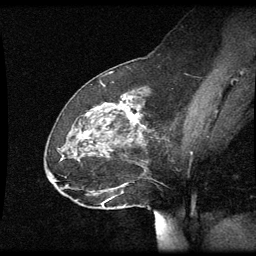
Breast MRI (dynamic contrast-enhanced), one sagittal slice; position 25 of 60 along the scan axis; dynamic contrast-enhanced series, image 2 of 3 at this slice position (ordered by acquisition); 1.5 T; TE 4.2 ms, TR 8.9 ms; 2 mm slice thickness; 256 × 256 image matrix, field of view 200 × 200 mm. Female patient, age 49 years. Case-level facts recorded for this patient, not image findings: setting: breast cancer imaged before/during neoadjuvant chemotherapy; receptor status: HR-positive, HER2-negative.
Structures marked on this image (semi-automatic segmentation, software-assisted and operator-edited):
- analysis volume of interest (the breast-tissue region the enhancement analysis was run in; not a lesion): box from (x=46, y=92) to (x=156, y=205) px
- tumour enhancement mask (voxels above the 70 % enhancement threshold inside the analysis volume of interest): (x=119, y=106)–(x=140, y=123)